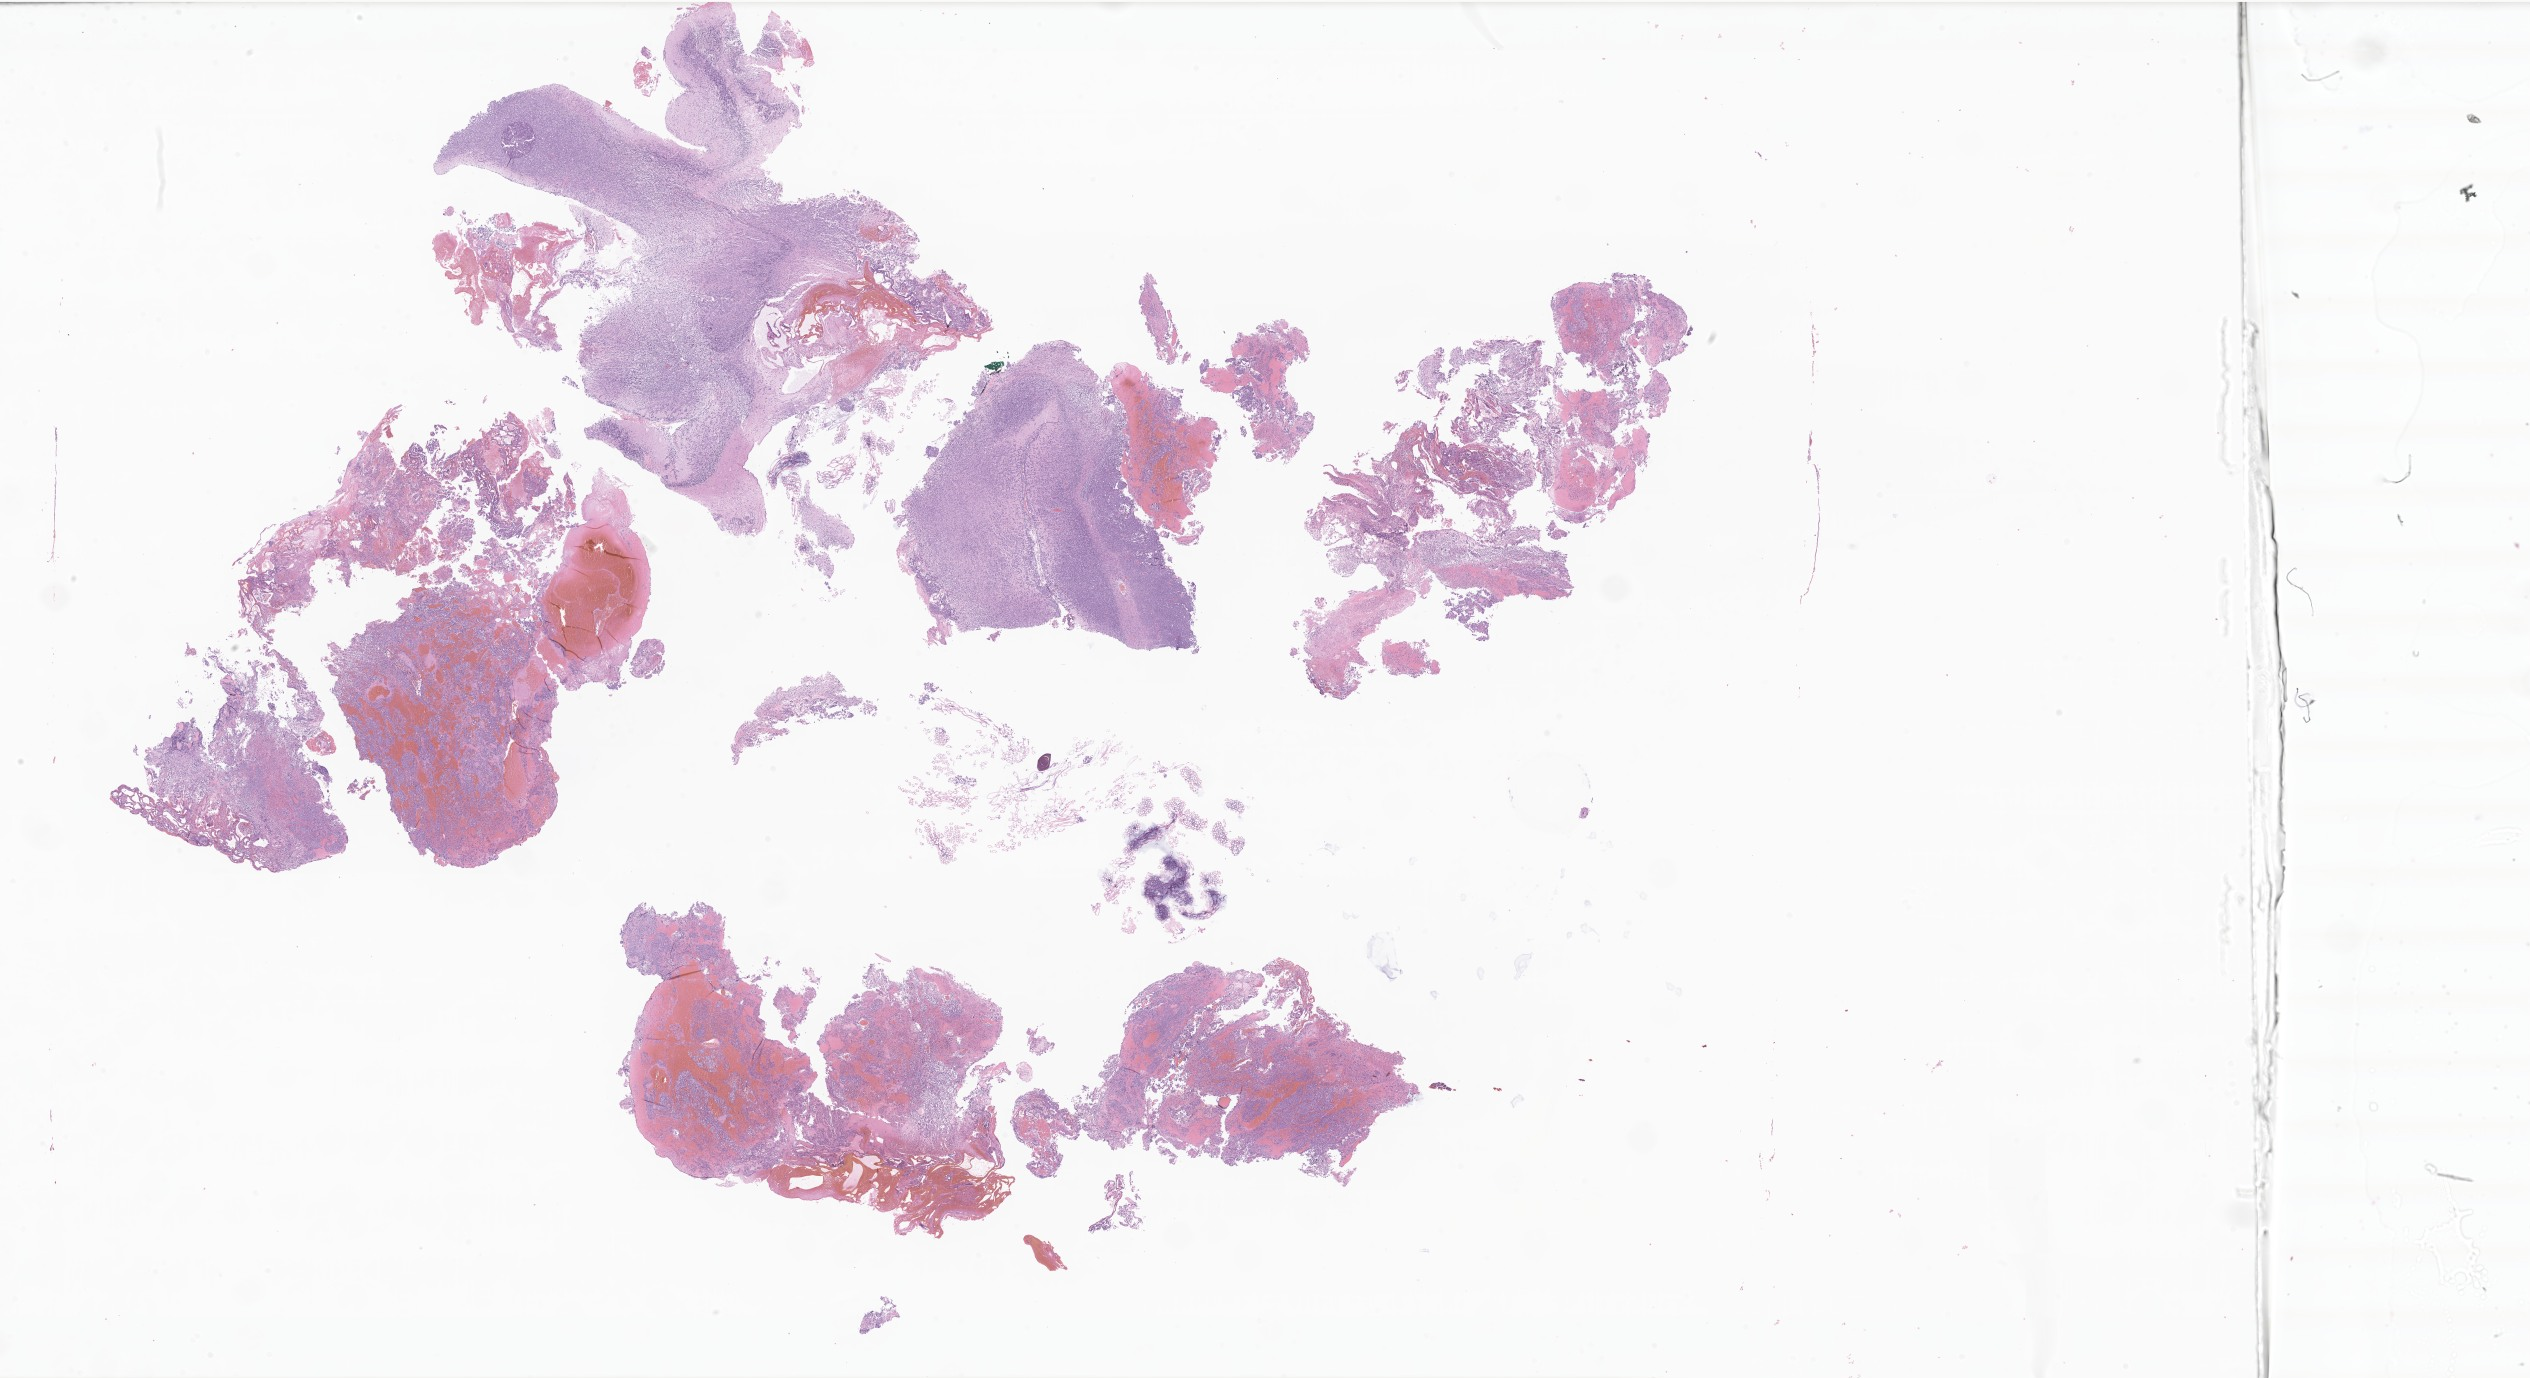
Hematoxylin and eosin (H&E) whole-slide image of tumor tissue from the cerebellum — a low-resolution overview of the entire scanned area, about 42.7 x 23.2 mm; formalin-fixed paraffin-embedded section. Female patient, age 97 months.
Diagnosis: Medulloblastoma, NOS.